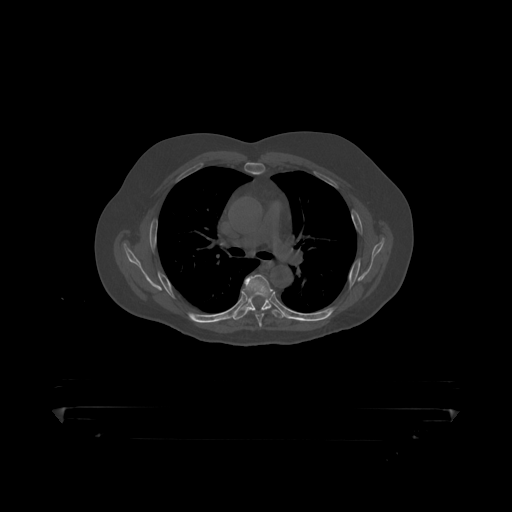
CT including the spine, one axial slice. Position 310 of 390 along the scan axis. Reconstruction kernel STANDARD. Bone window (W 1800 / L 400 HU). 1.25 mm slice thickness. 512 × 512 image matrix, field of view 650 × 650 mm. Male patient, age 60 years. From the clinical record (not read from this slice): primary cancer: prostate.
Annotated regions visible in this slice (semi-automatically segmented with operator editing):
- T5 vertebra: bounding box (x1, y1, x2, y2) in pixels: (243, 274, 273, 319)
- T6 vertebra: (235, 296, 282, 318)